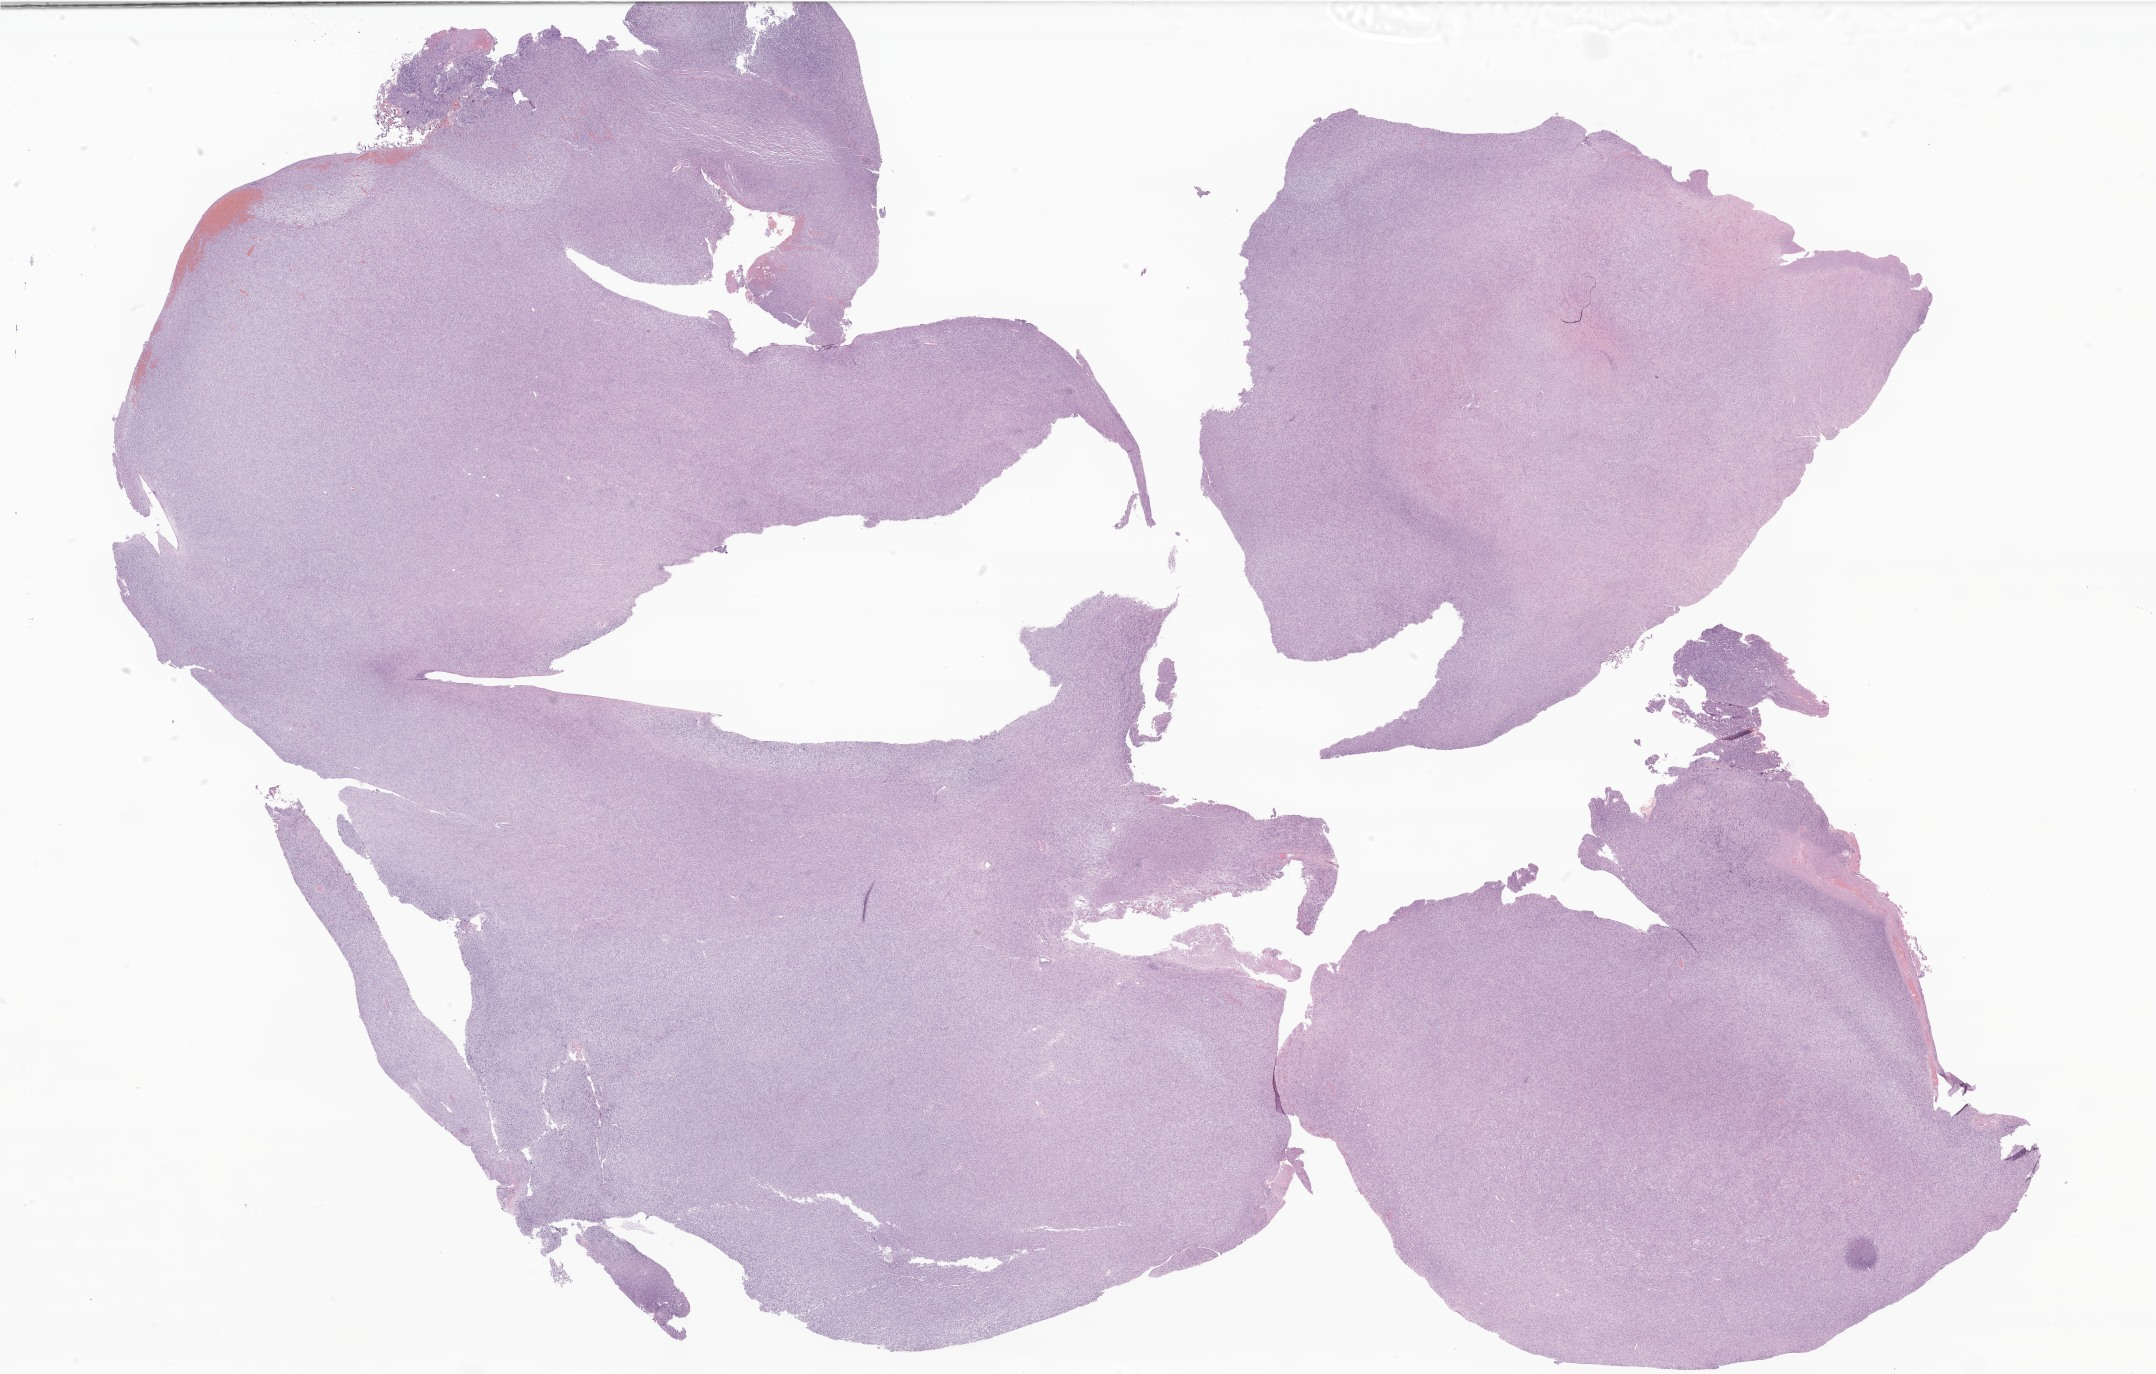
Haematoxylin and eosin whole-slide image of tumor tissue from the brain — a low-resolution overview of the entire scanned area, about 36.4 x 23.2 mm, formalin-fixed, paraffin-embedded (FFPE) tissue. Patient female; age 351 days.
Diagnosis: Ganglioglioma, NOS.